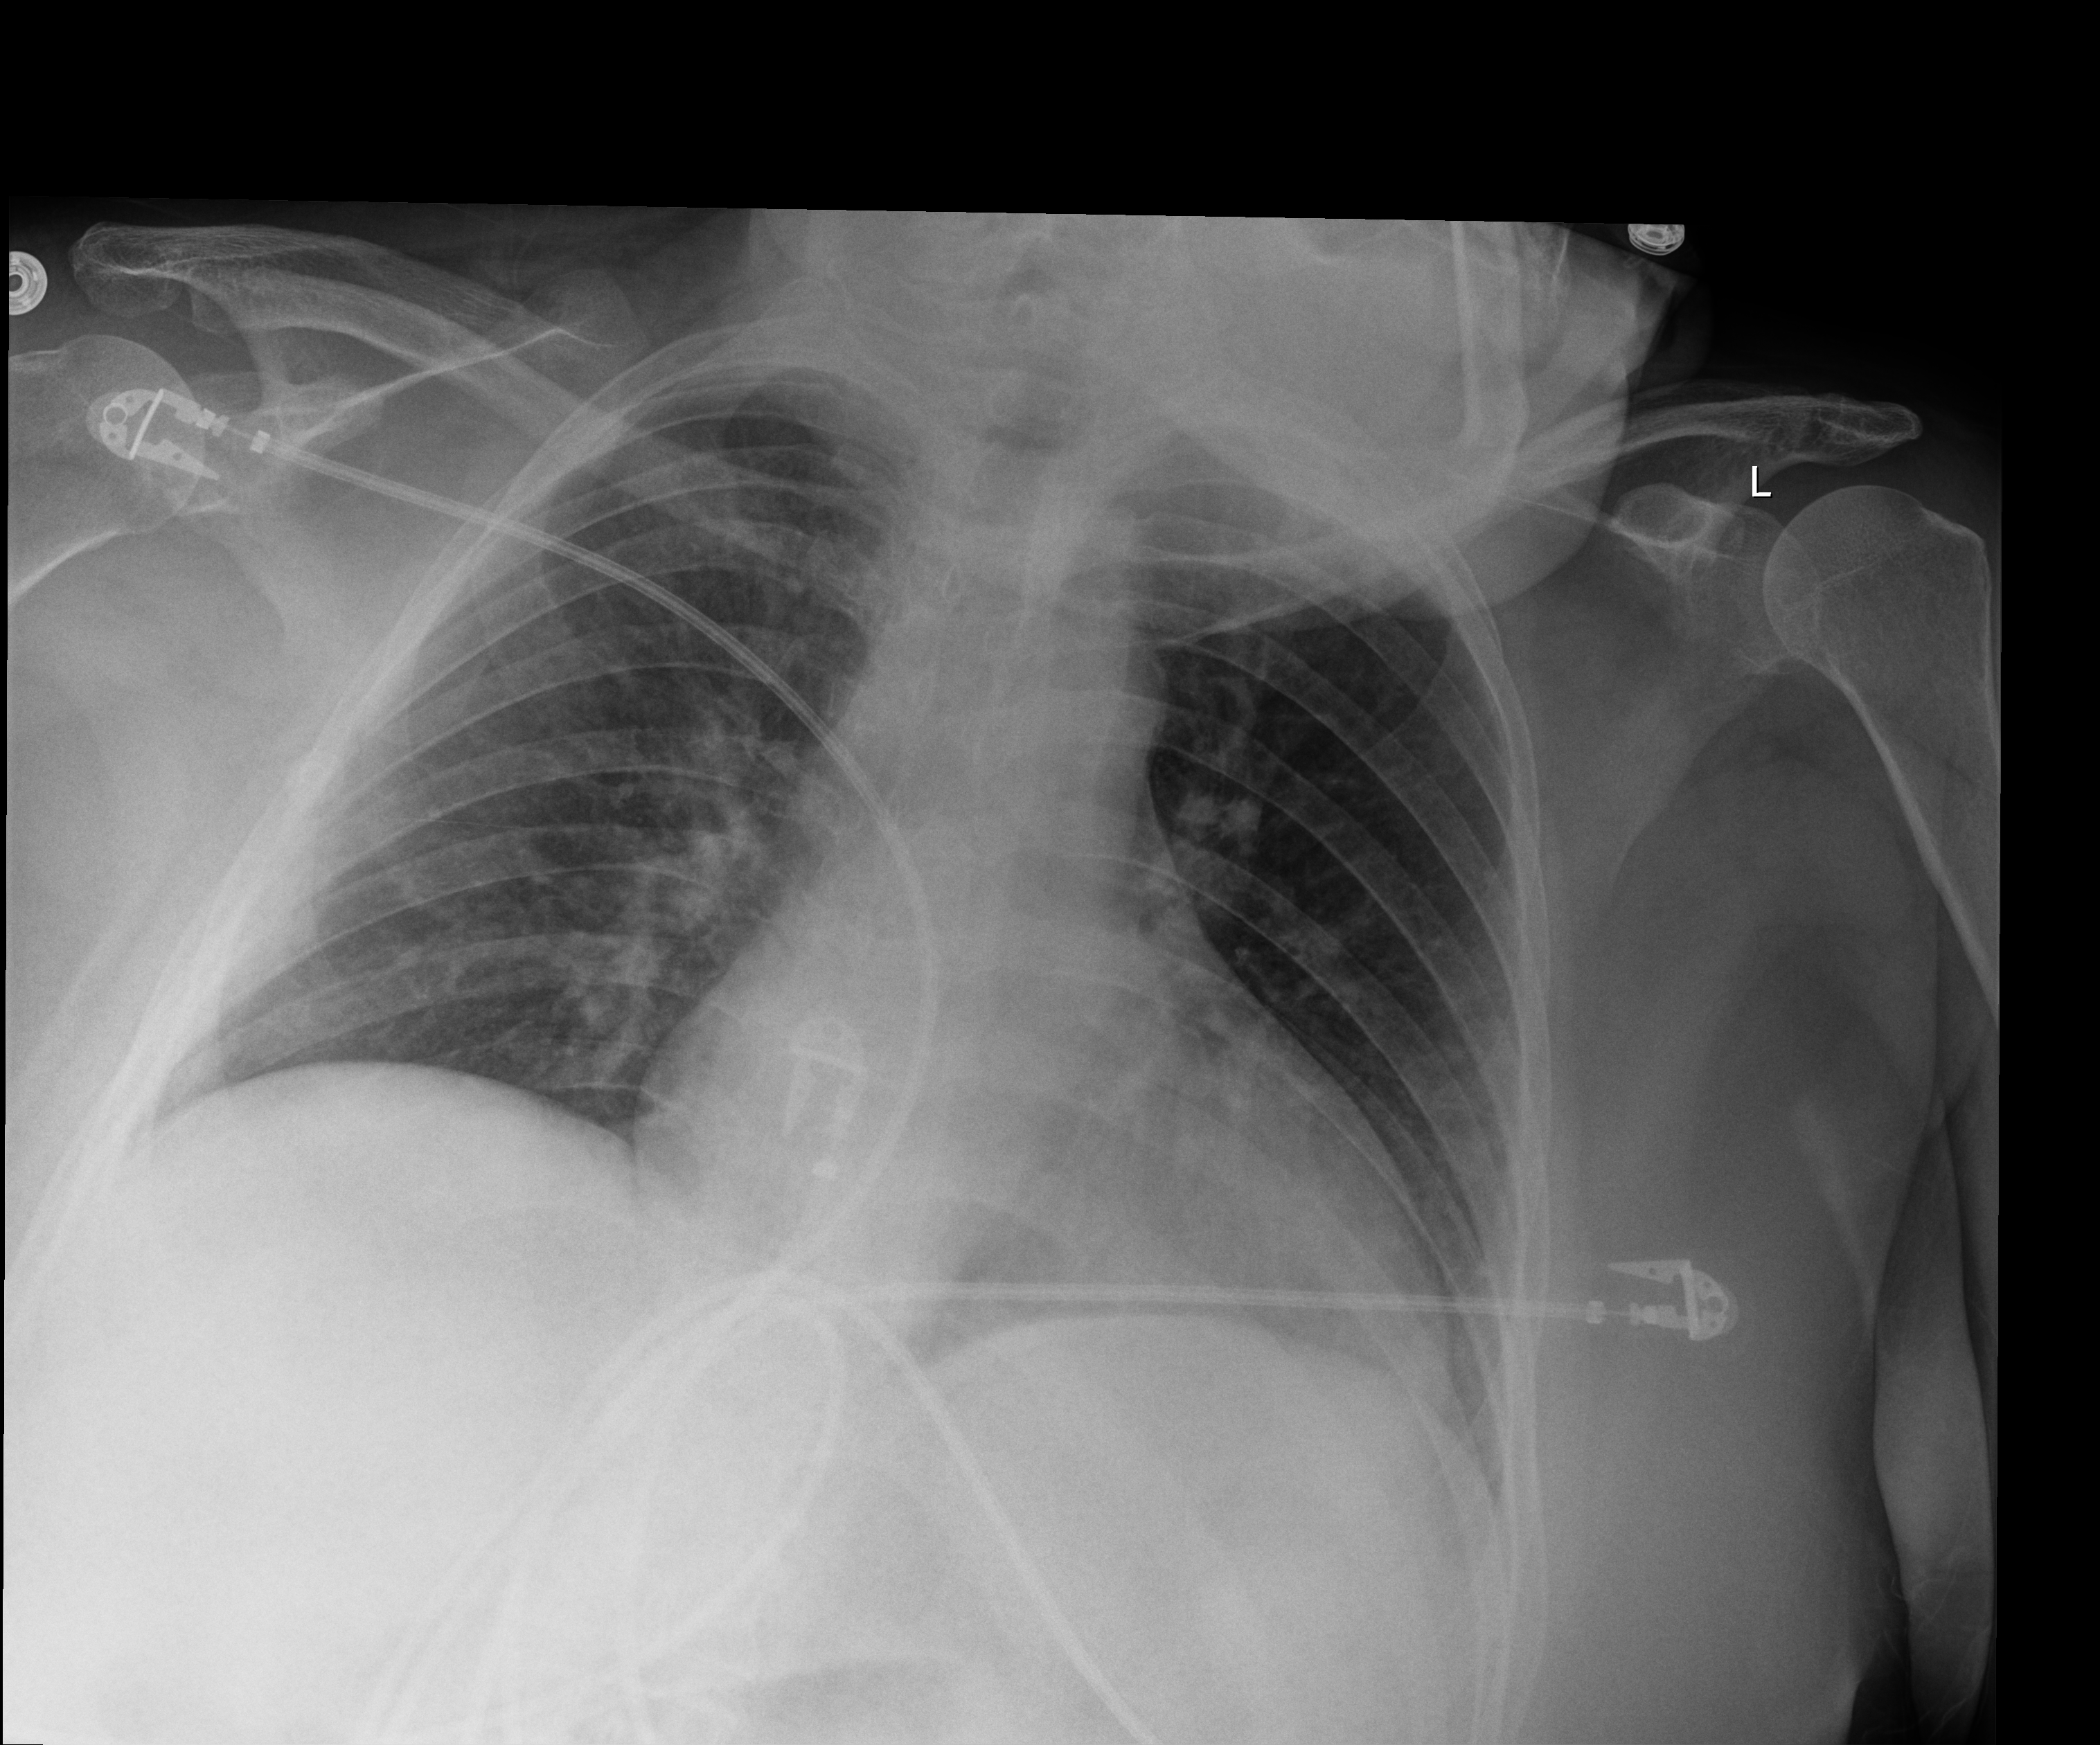
Chest X-ray (portable); anteroposterior (AP) projection. Patient hospitalised with COVID-19; female, aged 60–74 years.
From the hospital-stay record, not from the radiograph (when in the stay this image was taken is not recorded):
- length of hospital stay: 9 days